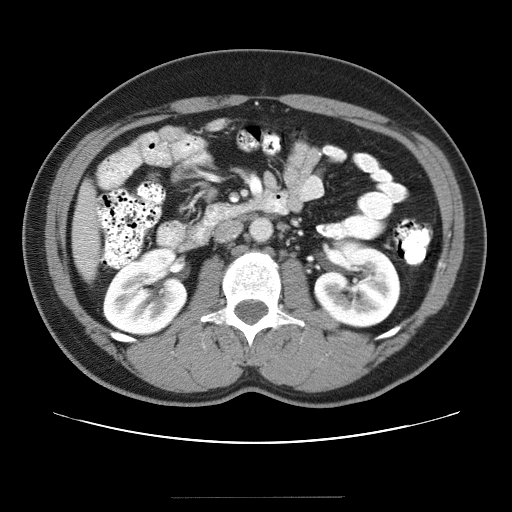
Contrast-enhanced abdominal CT (liver protocol), one axial slice; position 6 of 40 along the scan axis; reconstruction kernel STANDARD; 120 kVp; soft-tissue window (W 400 / L 40 HU); 5 mm slice thickness; 512 × 512 image matrix, field of view 380 × 380 mm. Case-level facts recorded for this patient, not image findings: diagnosis: hepatocellular carcinoma (patient treated with transarterial chemoembolisation; whether this scan precedes or follows treatment is not stated here); TNM stage (as recorded): Stage-IVA; Child-Pugh class: B; tumour nodularity: multinodular.
Structures marked on this image (semi-automatic segmentation, software-assisted and operator-edited):
- liver parenchyma outside the tumour (the mass and vessels are separate outlines, so this box may not span the whole liver): bounding box [x1, y1, x2, y2] px = [72, 180, 100, 276]
- liver vessels: [98, 211, 100, 214]